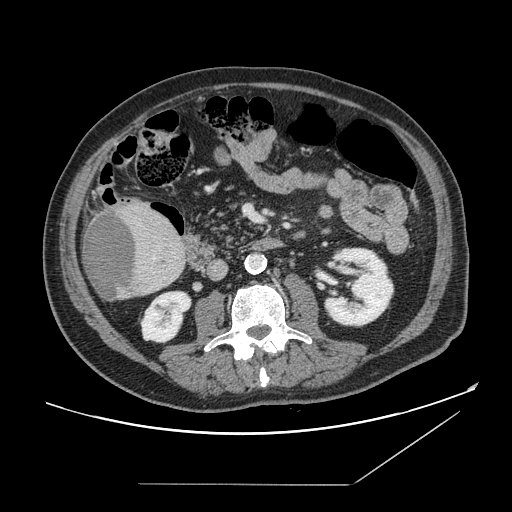
Contrast-enhanced abdominal CT, one axial slice. Slice 48 of 166 in the series (ordered by position). 120 kVp. Soft-tissue window (W 400 / L 40 HU). 2.5 mm slice thickness. 512 × 512 image matrix, field of view 416 × 416 mm. Male patient, age 80 years. From the clinical record (not read from this slice): diagnosis: colorectal cancer liver metastases, imaged before liver resection; multiple liver metastases: no; largest metastasis: 2.2 cm; disease in both lobes: no.
Annotated regions visible in this slice (manually delineated by an expert):
- liver: bounding box <82,201,187,301> (left, top, right, bottom; pixels)
- liver metastasis: <85,208,138,302>